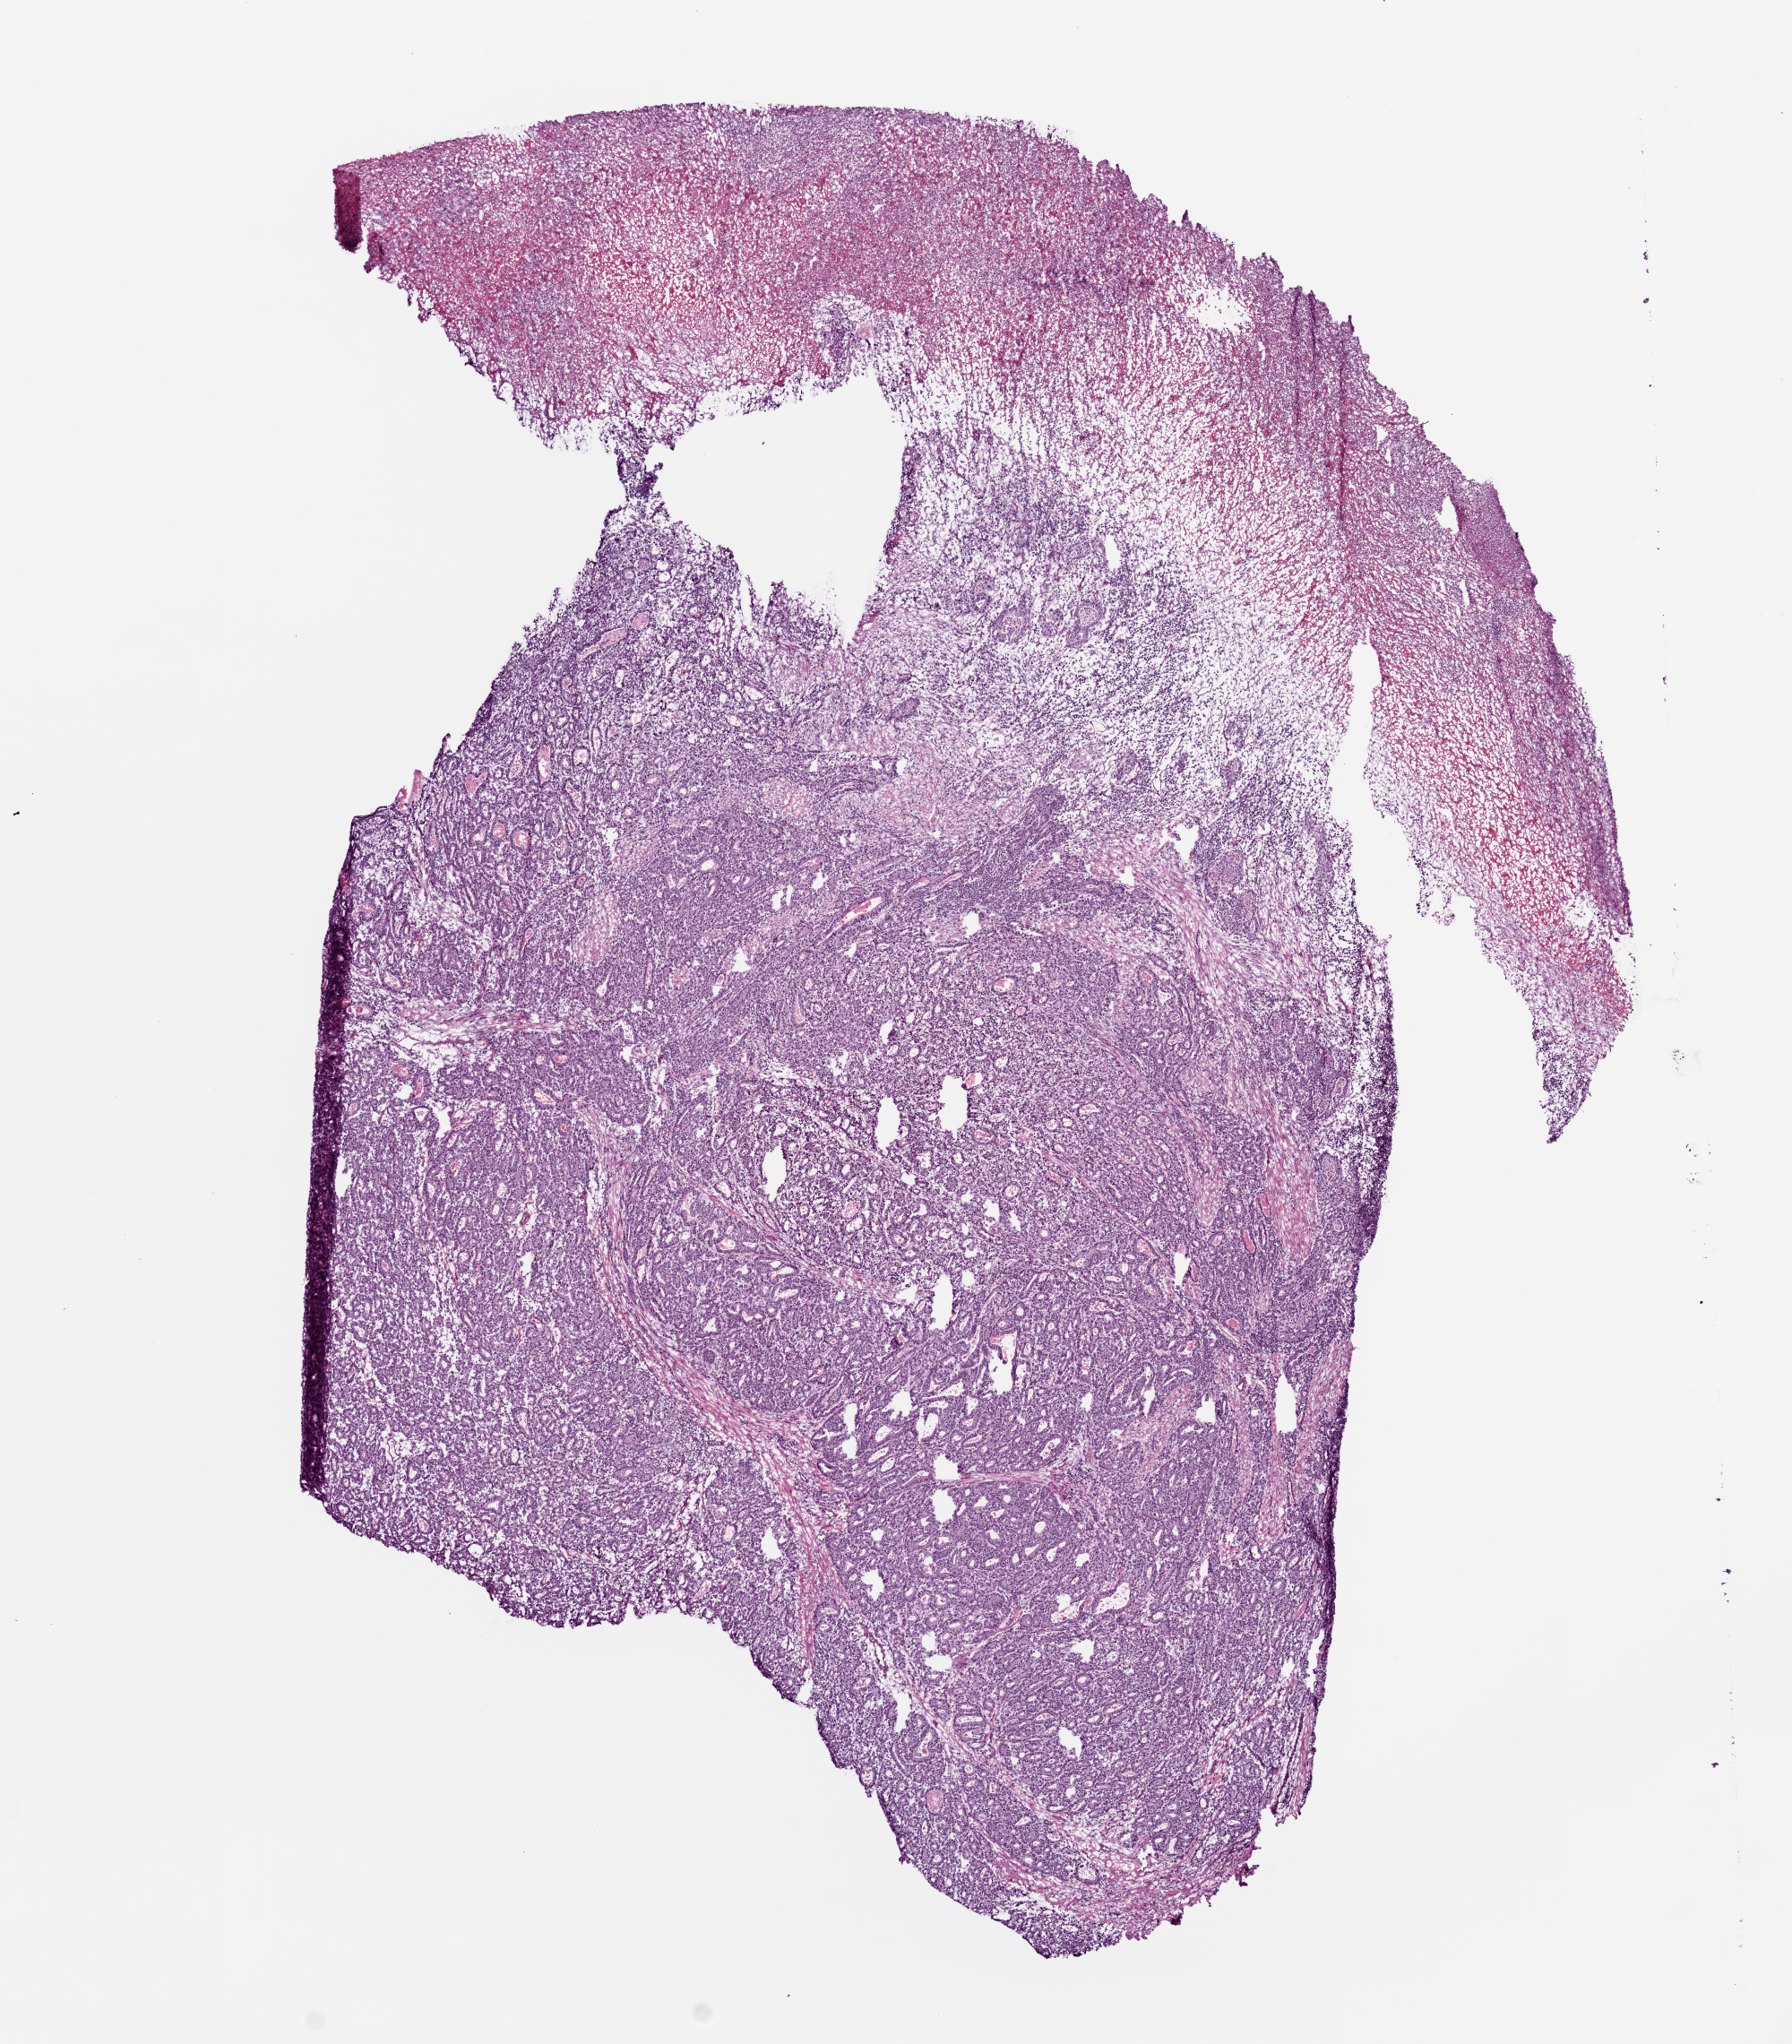
Digitized H&E-stained tissue section (whole slide) — whole scanned area (about 8.0 x 9.2 mm, from a 20x scan) shown as a low-resolution overview; frozen section from the top of the tissue portion; sample: primary tumour, stomach. Patient: female, age at initial diagnosis 78 years. Histologic grade: G2 (moderately differentiated). Composition of this section per pathologist review: tumour cells 70%, tumour nuclei 75%, normal cells 0%, stromal cells 10%, necrosis 20%.
AJCC pathologic stage: II. Lymph nodes positive (case pathology): 3 of 39 examined. Histologic diagnosis: Adenocarcinoma, intestinal type. TNM: T2b N1 M0.